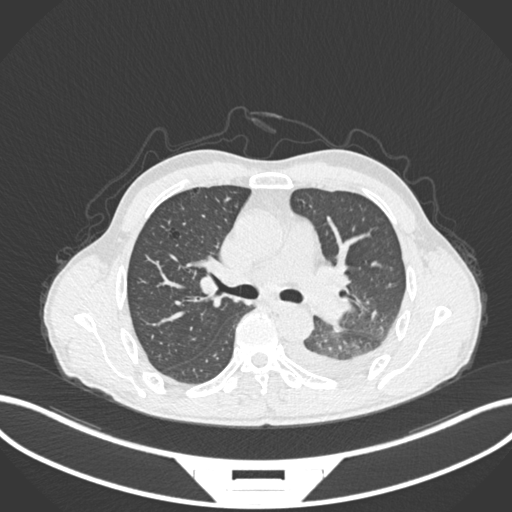
Chest CT, one axial slice; position 156 of 222 along the scan axis; reconstruction kernel B30f; 120 kVp; lung window (W 1500 / L -600 HU); 512 × 512 image matrix, field of view 400 × 400 mm. Patient: male, 47 years. From the clinical record (not read from this slice): clinical TNM (as recorded): T3 N1 M1c.
Outlined on this slice (bounding box drawn by a radiologist):
- lung tumour (recorded histology: small cell carcinoma): box from (x=317, y=296) to (x=352, y=324) px